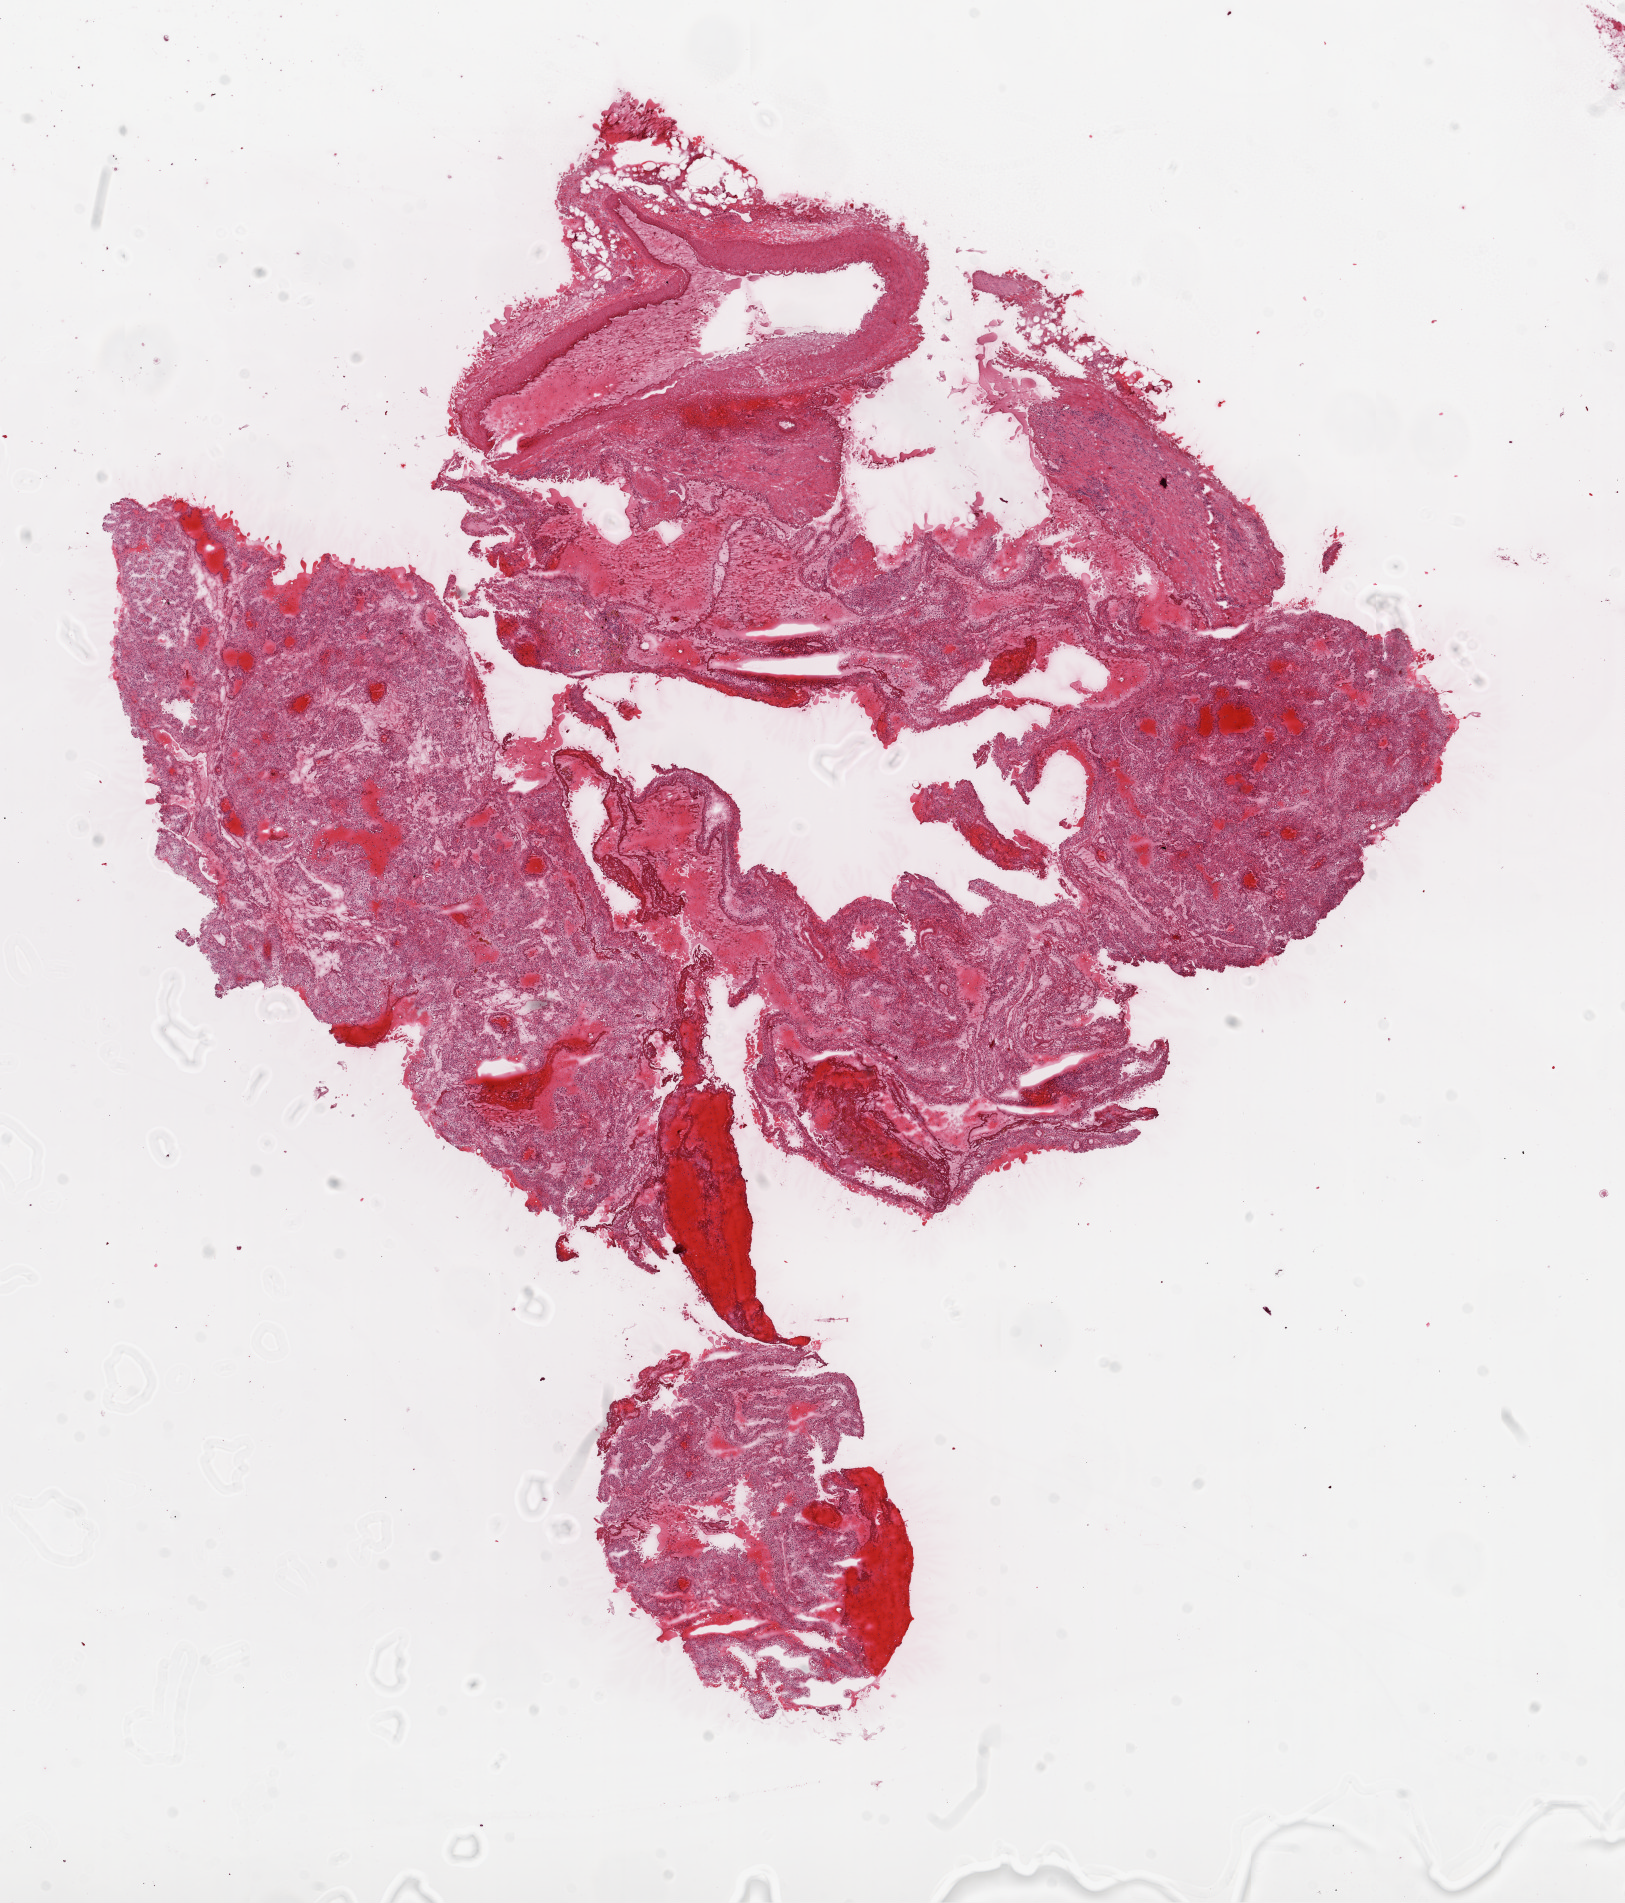
Digitized H&E-stained tissue section (whole slide), shown as a low-resolution overview of the whole scanned area (about 13.0 x 15.3 mm). Frozen section from the top of the tissue portion. Kidney, primary tumour sample. Patient: male, age at initial diagnosis 46 years. Histologic grade: G2 (moderately differentiated). Composition of this section per pathologist review: tumour cells 80%, tumour nuclei 80%, normal cells 5%, stromal cells 15%, necrosis 0%.
AJCC pathologic stage: I. Laterality: right. Pathologic diagnosis: Clear cell adenocarcinoma, NOS.